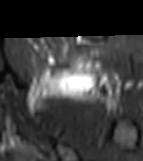
MRI of an extremity soft-tissue mass, one axial slice. Slice 44 of 81 in the series (ordered by position). STIR. MR volume resampled by the dataset authors to the PET/CT grid (not the native acquisition matrix). 3.27 mm slice thickness. 143 × 161 image matrix, field of view 140 × 157 mm. Female patient. From the clinical record (not read from this slice): histological type: myxofibrosarcoma; grade: intermediate; site of the primary tumour: left thigh.
Outlined on this slice (expert contour drawn on MRI and transferred to this co-registered scan by the dataset authors):
- gross tumour volume including surrounding oedema: bounding box [x1, y1, x2, y2] px = [24, 60, 123, 111]
- gross tumour volume (mass): [47, 60, 91, 93]